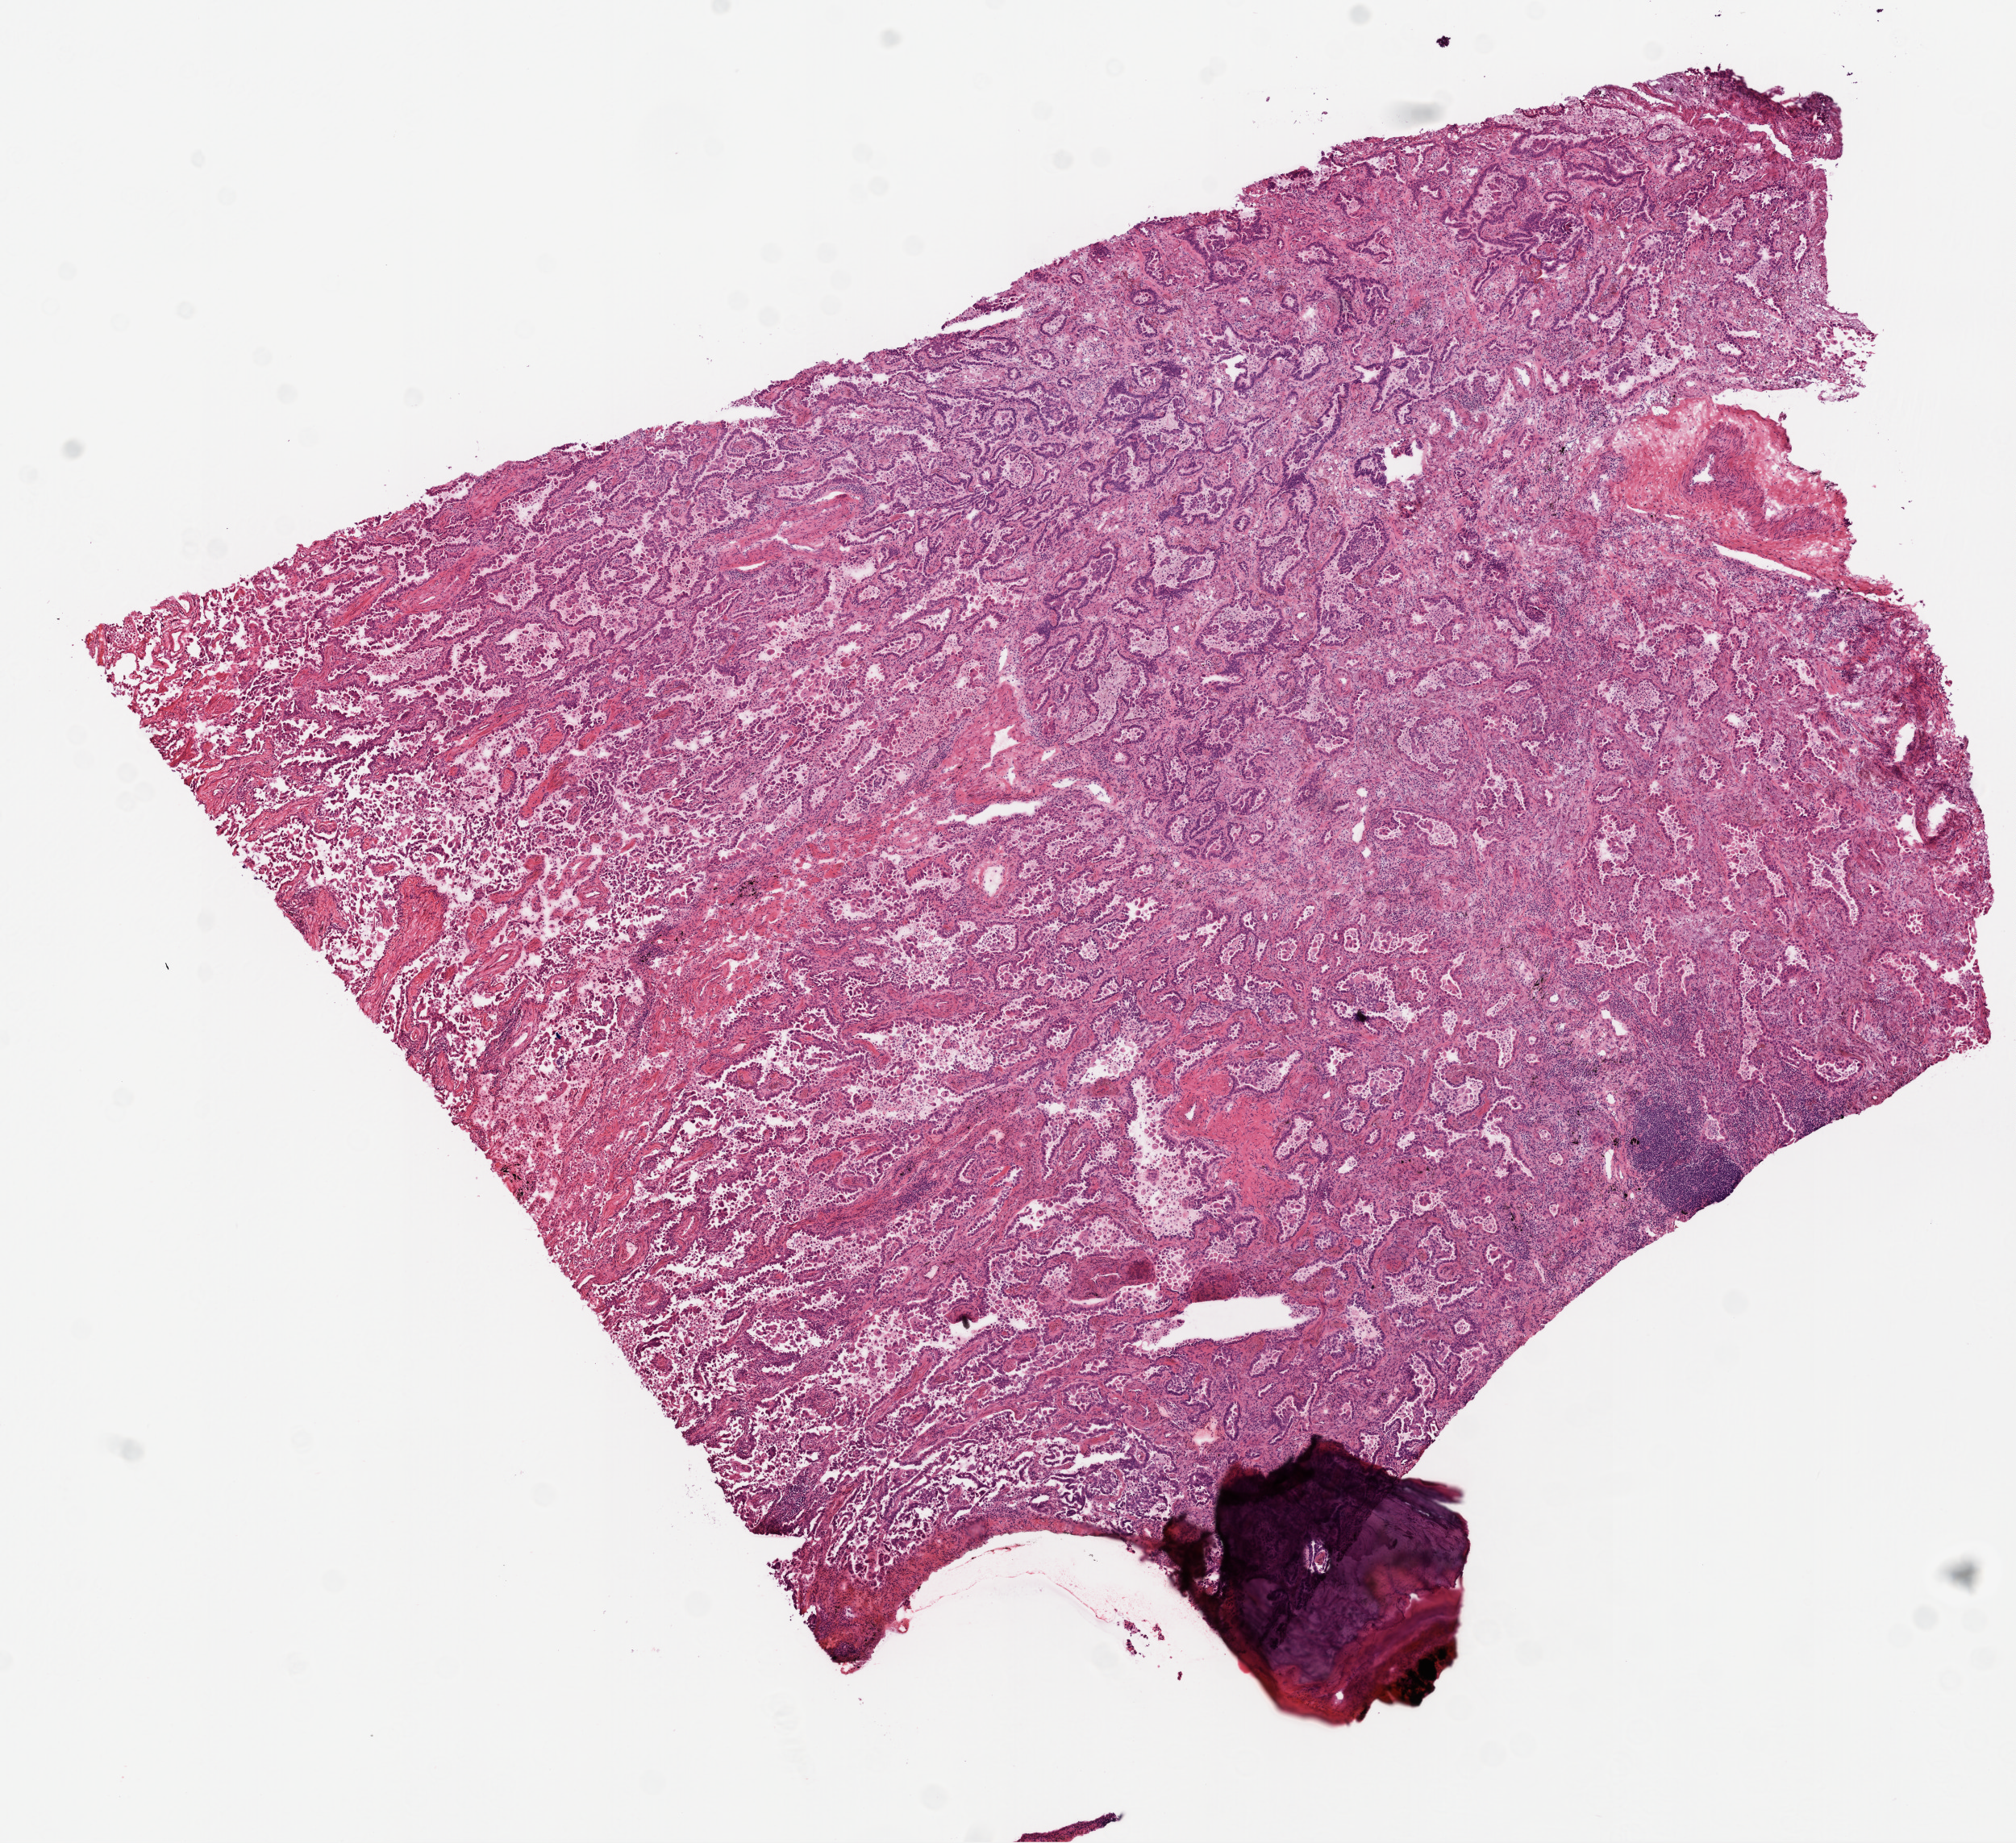
Hematoxylin and eosin (H&E) stained whole-slide image, shown as a low-resolution overview of the whole scanned area (about 10.0 x 9.2 mm, slide scanned at 20x); frozen section; sample: primary tumour, lung. Patient: female, age at initial diagnosis 61 years. Pathologist review of this section (percent, as recorded): tumour cells 85%, tumour nuclei 70%, normal cells 0%, stromal cells 15%, necrosis 0%.
AJCC pathologic stage: IIB (4th edition). Laterality: right. Diagnosis: Adenocarcinoma, NOS (lower lobe, lung).